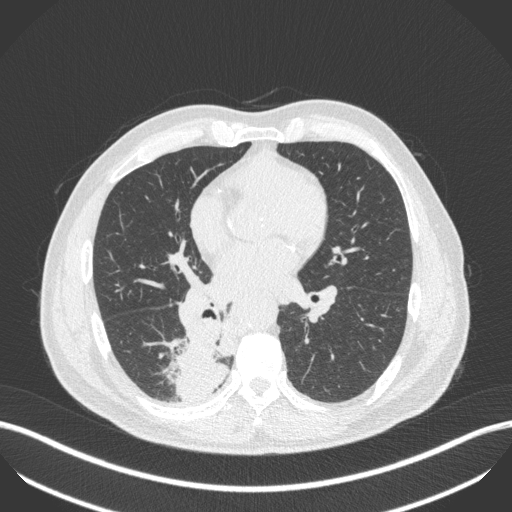
Chest CT, one axial slice; position 227 of 451 along the scan axis; reconstruction kernel B31f; 100 kVp; lung window (W 1500 / L -600 HU); 512 × 512 image matrix. Patient: male, 61 years. Case-level facts recorded for this patient, not image findings: clinical TNM (as recorded): T1 N0 M0.
Structures marked on this image (rectangle marked by the reading radiologist):
- lung tumour (recorded histology: small cell carcinoma): bounding box (x1, y1, x2, y2) in pixels: (162, 320, 228, 403)